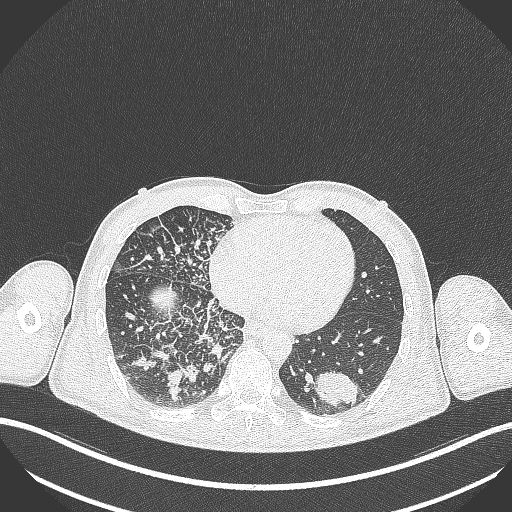
Chest CT, one axial slice. Position 104 of 348 along the scan axis. Reconstruction kernel B70f. 120 kVp. Lung window (W 1500 / L -600 HU). 1 mm slice thickness. 512 × 512 image matrix, field of view 400 × 400 mm. Patient: male, 49 years. Case-level facts recorded for this patient, not image findings: clinical TNM (as recorded): T2b N1 M0.
Annotated regions visible in this slice (bounding box drawn by a radiologist):
- lung tumour (recorded histology: adenocarcinoma): box from (x=315, y=365) to (x=364, y=408) px